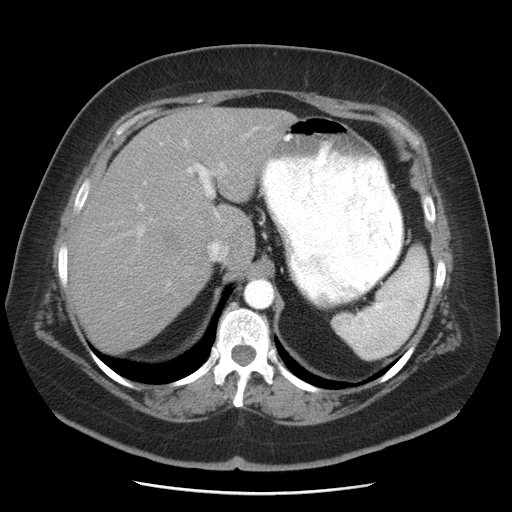
Contrast-enhanced abdominal CT, one axial slice; position 35 of 55 along the scan axis; 120 kVp; intravenous contrast given; soft-tissue window (W 400 / L 40 HU); 5 mm slice thickness; 512 × 512 image matrix, field of view 380 × 380 mm. Female patient, age 52 years. Case-level facts recorded for this patient, not image findings: diagnosis: colorectal cancer liver metastases, imaged before liver resection; multiple liver metastases: yes; largest metastasis: 2.5 cm; disease in both lobes: yes.
Structures marked on this image (manually delineated by an expert):
- hepatic veins: bounding box (x1, y1, x2, y2) in pixels: (208, 241, 230, 260)
- liver: (68, 108, 297, 354)
- planned liver remnant (the part of the liver to remain after resection): (68, 169, 211, 354)
- portal vein (with intrahepatic branches): (125, 126, 260, 284)